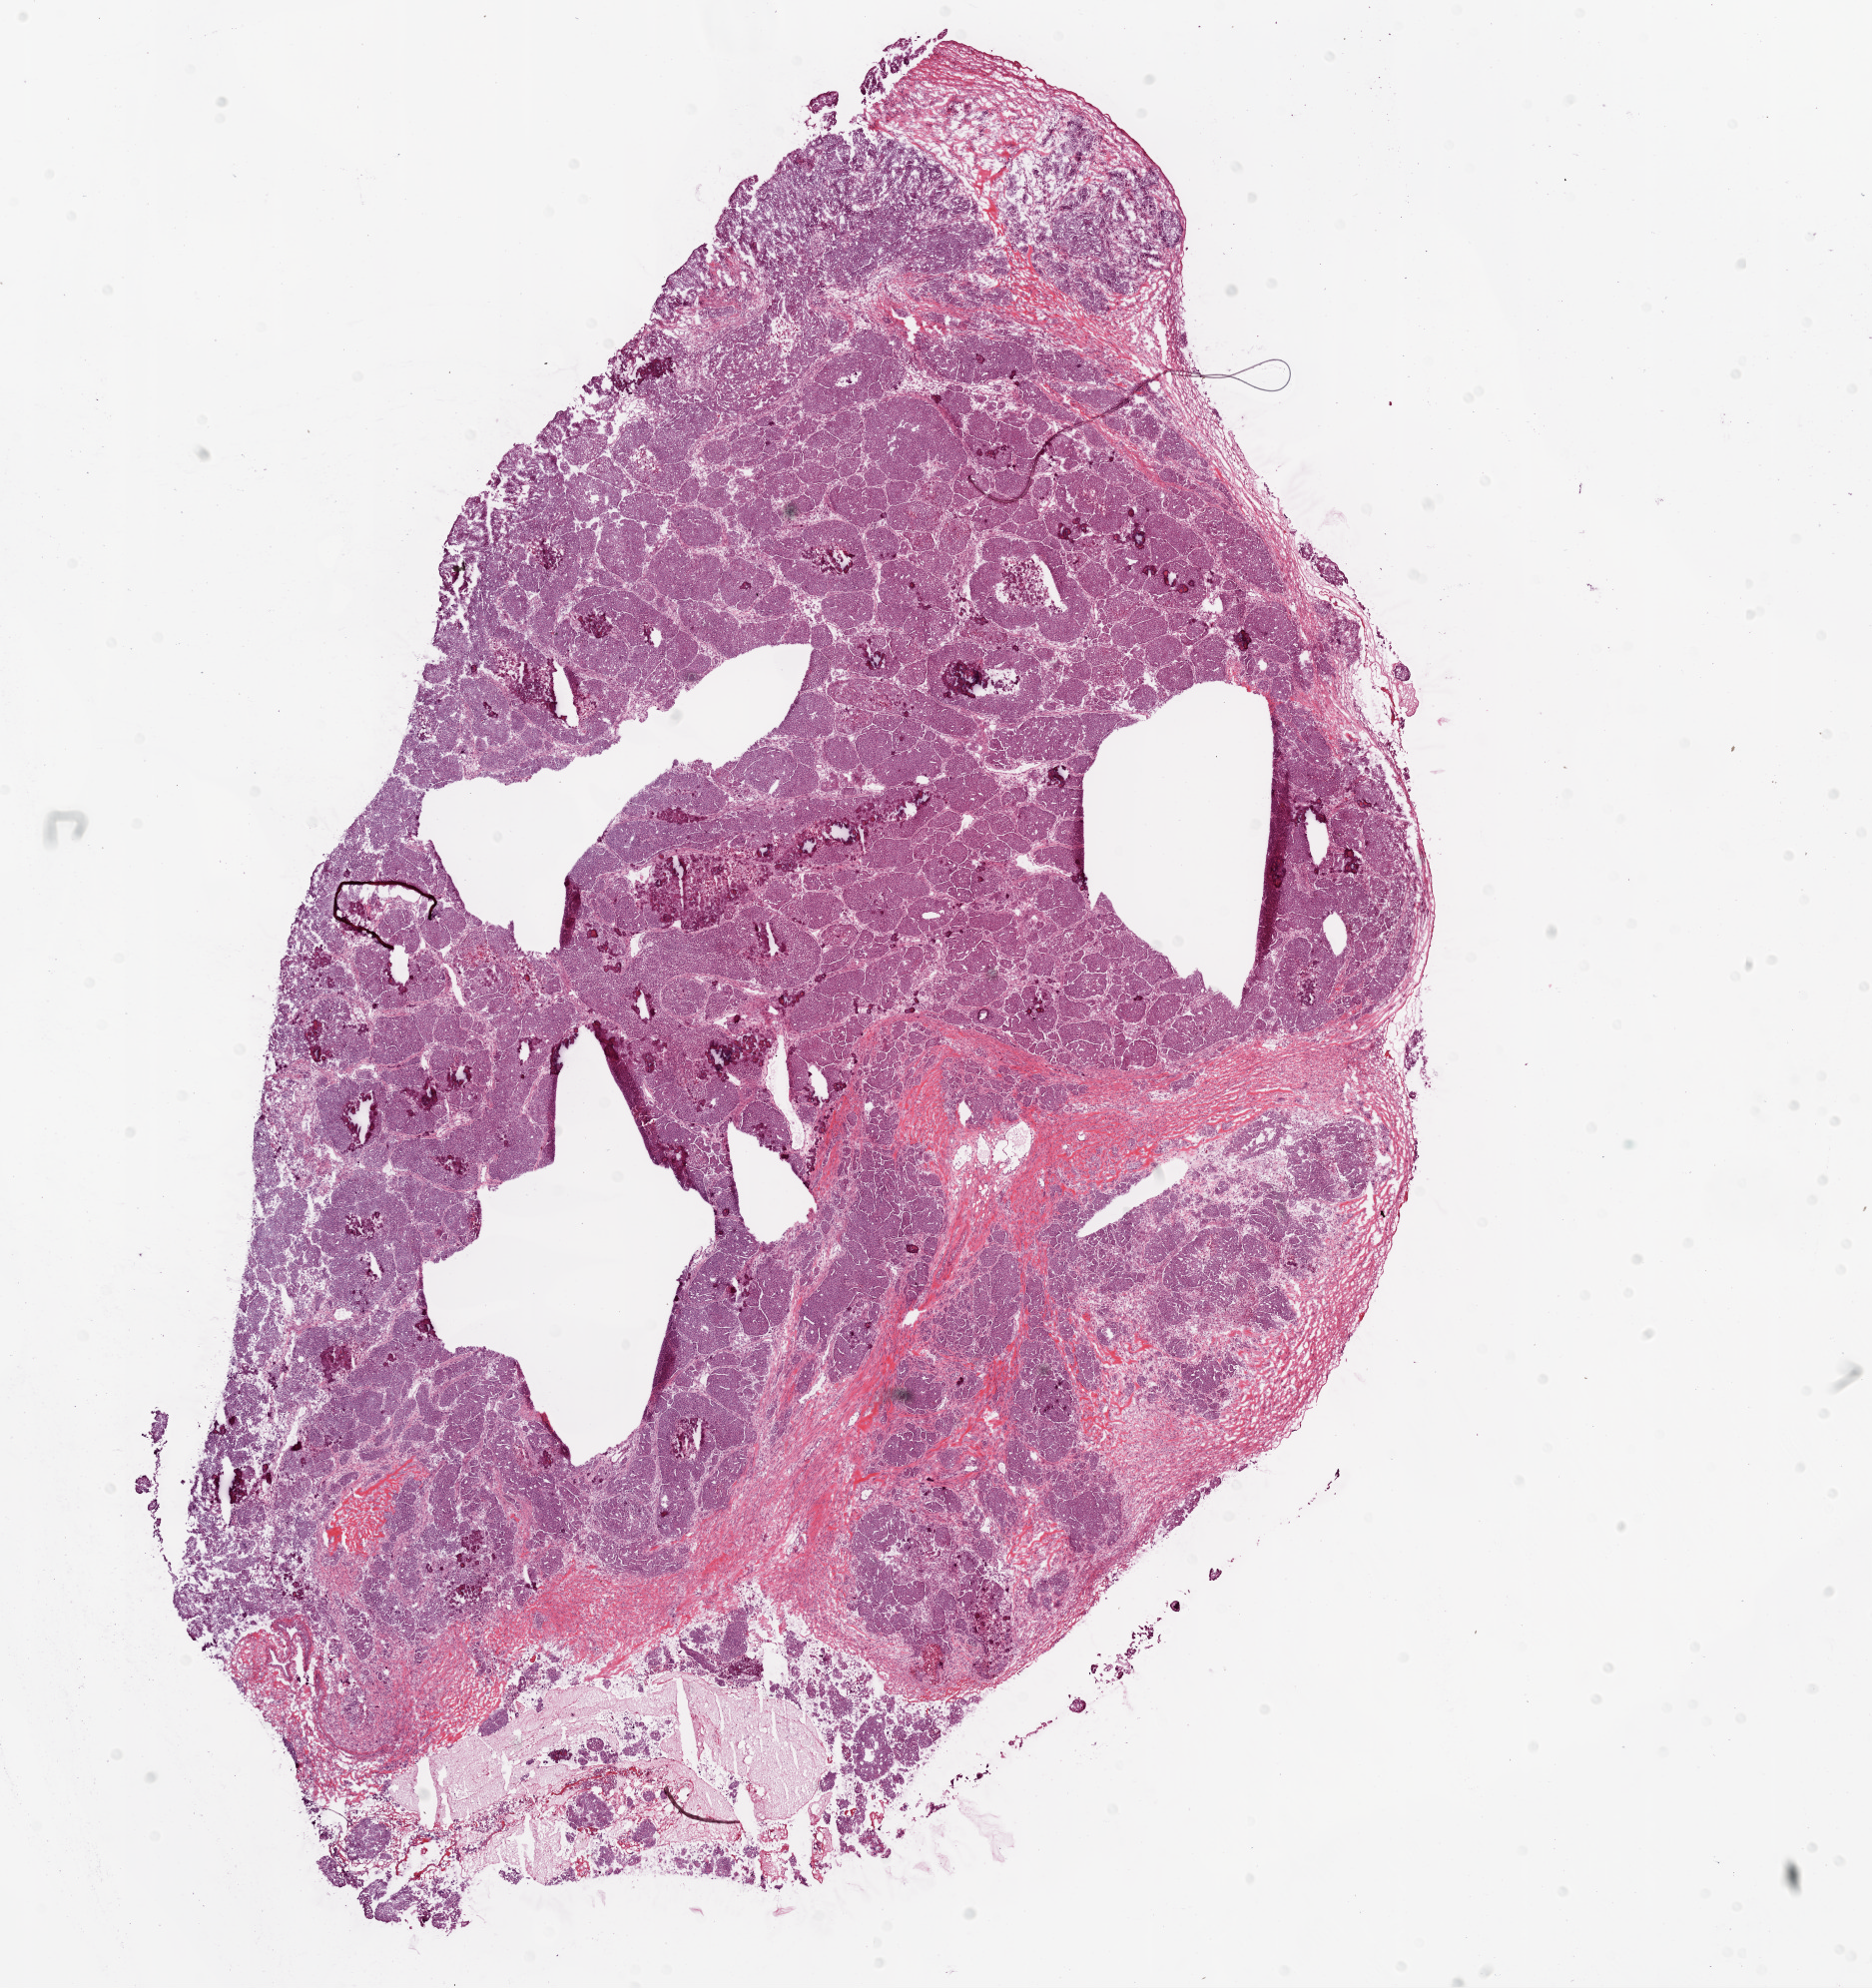
H&E-stained whole-slide image — whole scanned area (about 15.0 x 16.0 mm, from a 20x scan) shown as a low-resolution overview, frozen section from the bottom of the tissue portion, ovary, primary tumour sample. Female, age 72 years at initial diagnosis. Histologic grade: G3 (poorly differentiated). Pathologist review of this section (percent, as recorded): tumour cells 98%, tumour nuclei 90%, normal cells 0%, stromal cells 0%, necrosis 2%.
* histologic diagnosis: Serous cystadenocarcinoma, NOS
* FIGO stage: IIIC